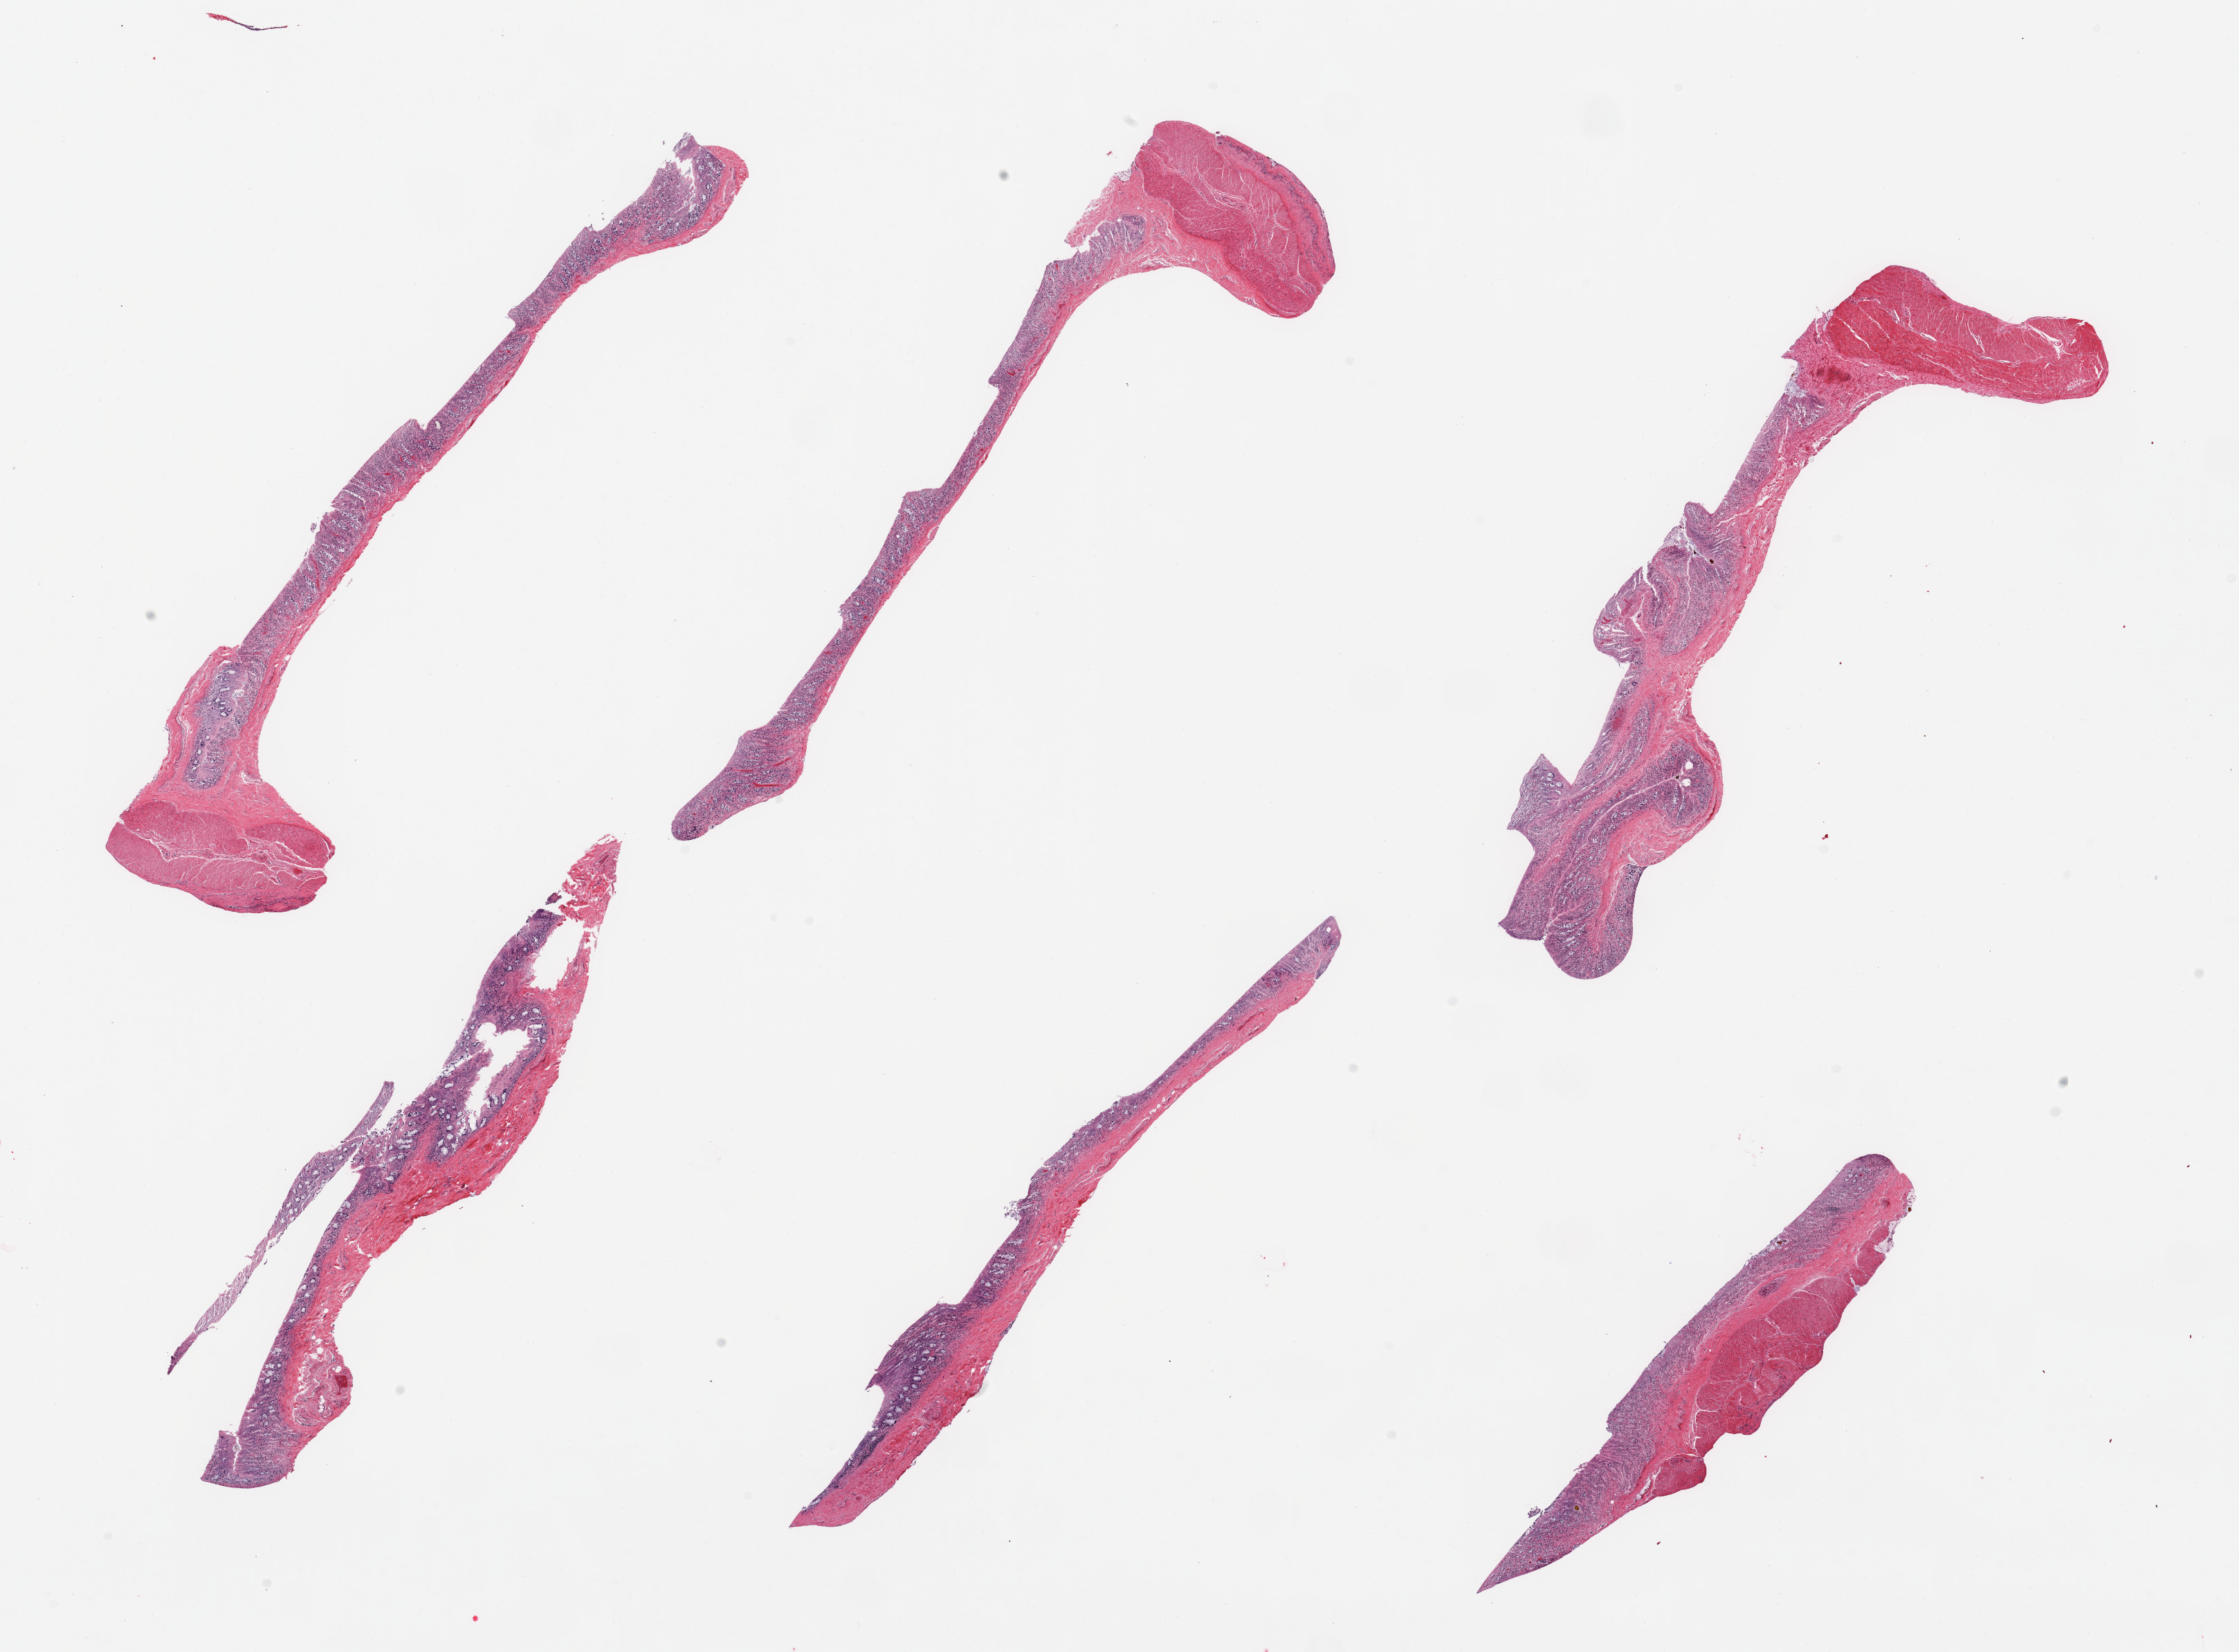
Haematoxylin and eosin whole-slide image, brightfield, shown as a low-resolution overview of the whole scanned area (about 25.6 x 18.9 mm, slide scanned at 20x); PAXgene-fixed paraffin-embedded (PFPE) section; sampled site (target tissue): transverse colon; tissue donor sample. Donor: male.
• pathologist's review note for this sample: 6 pieces, target mucosa markedly autolyzed